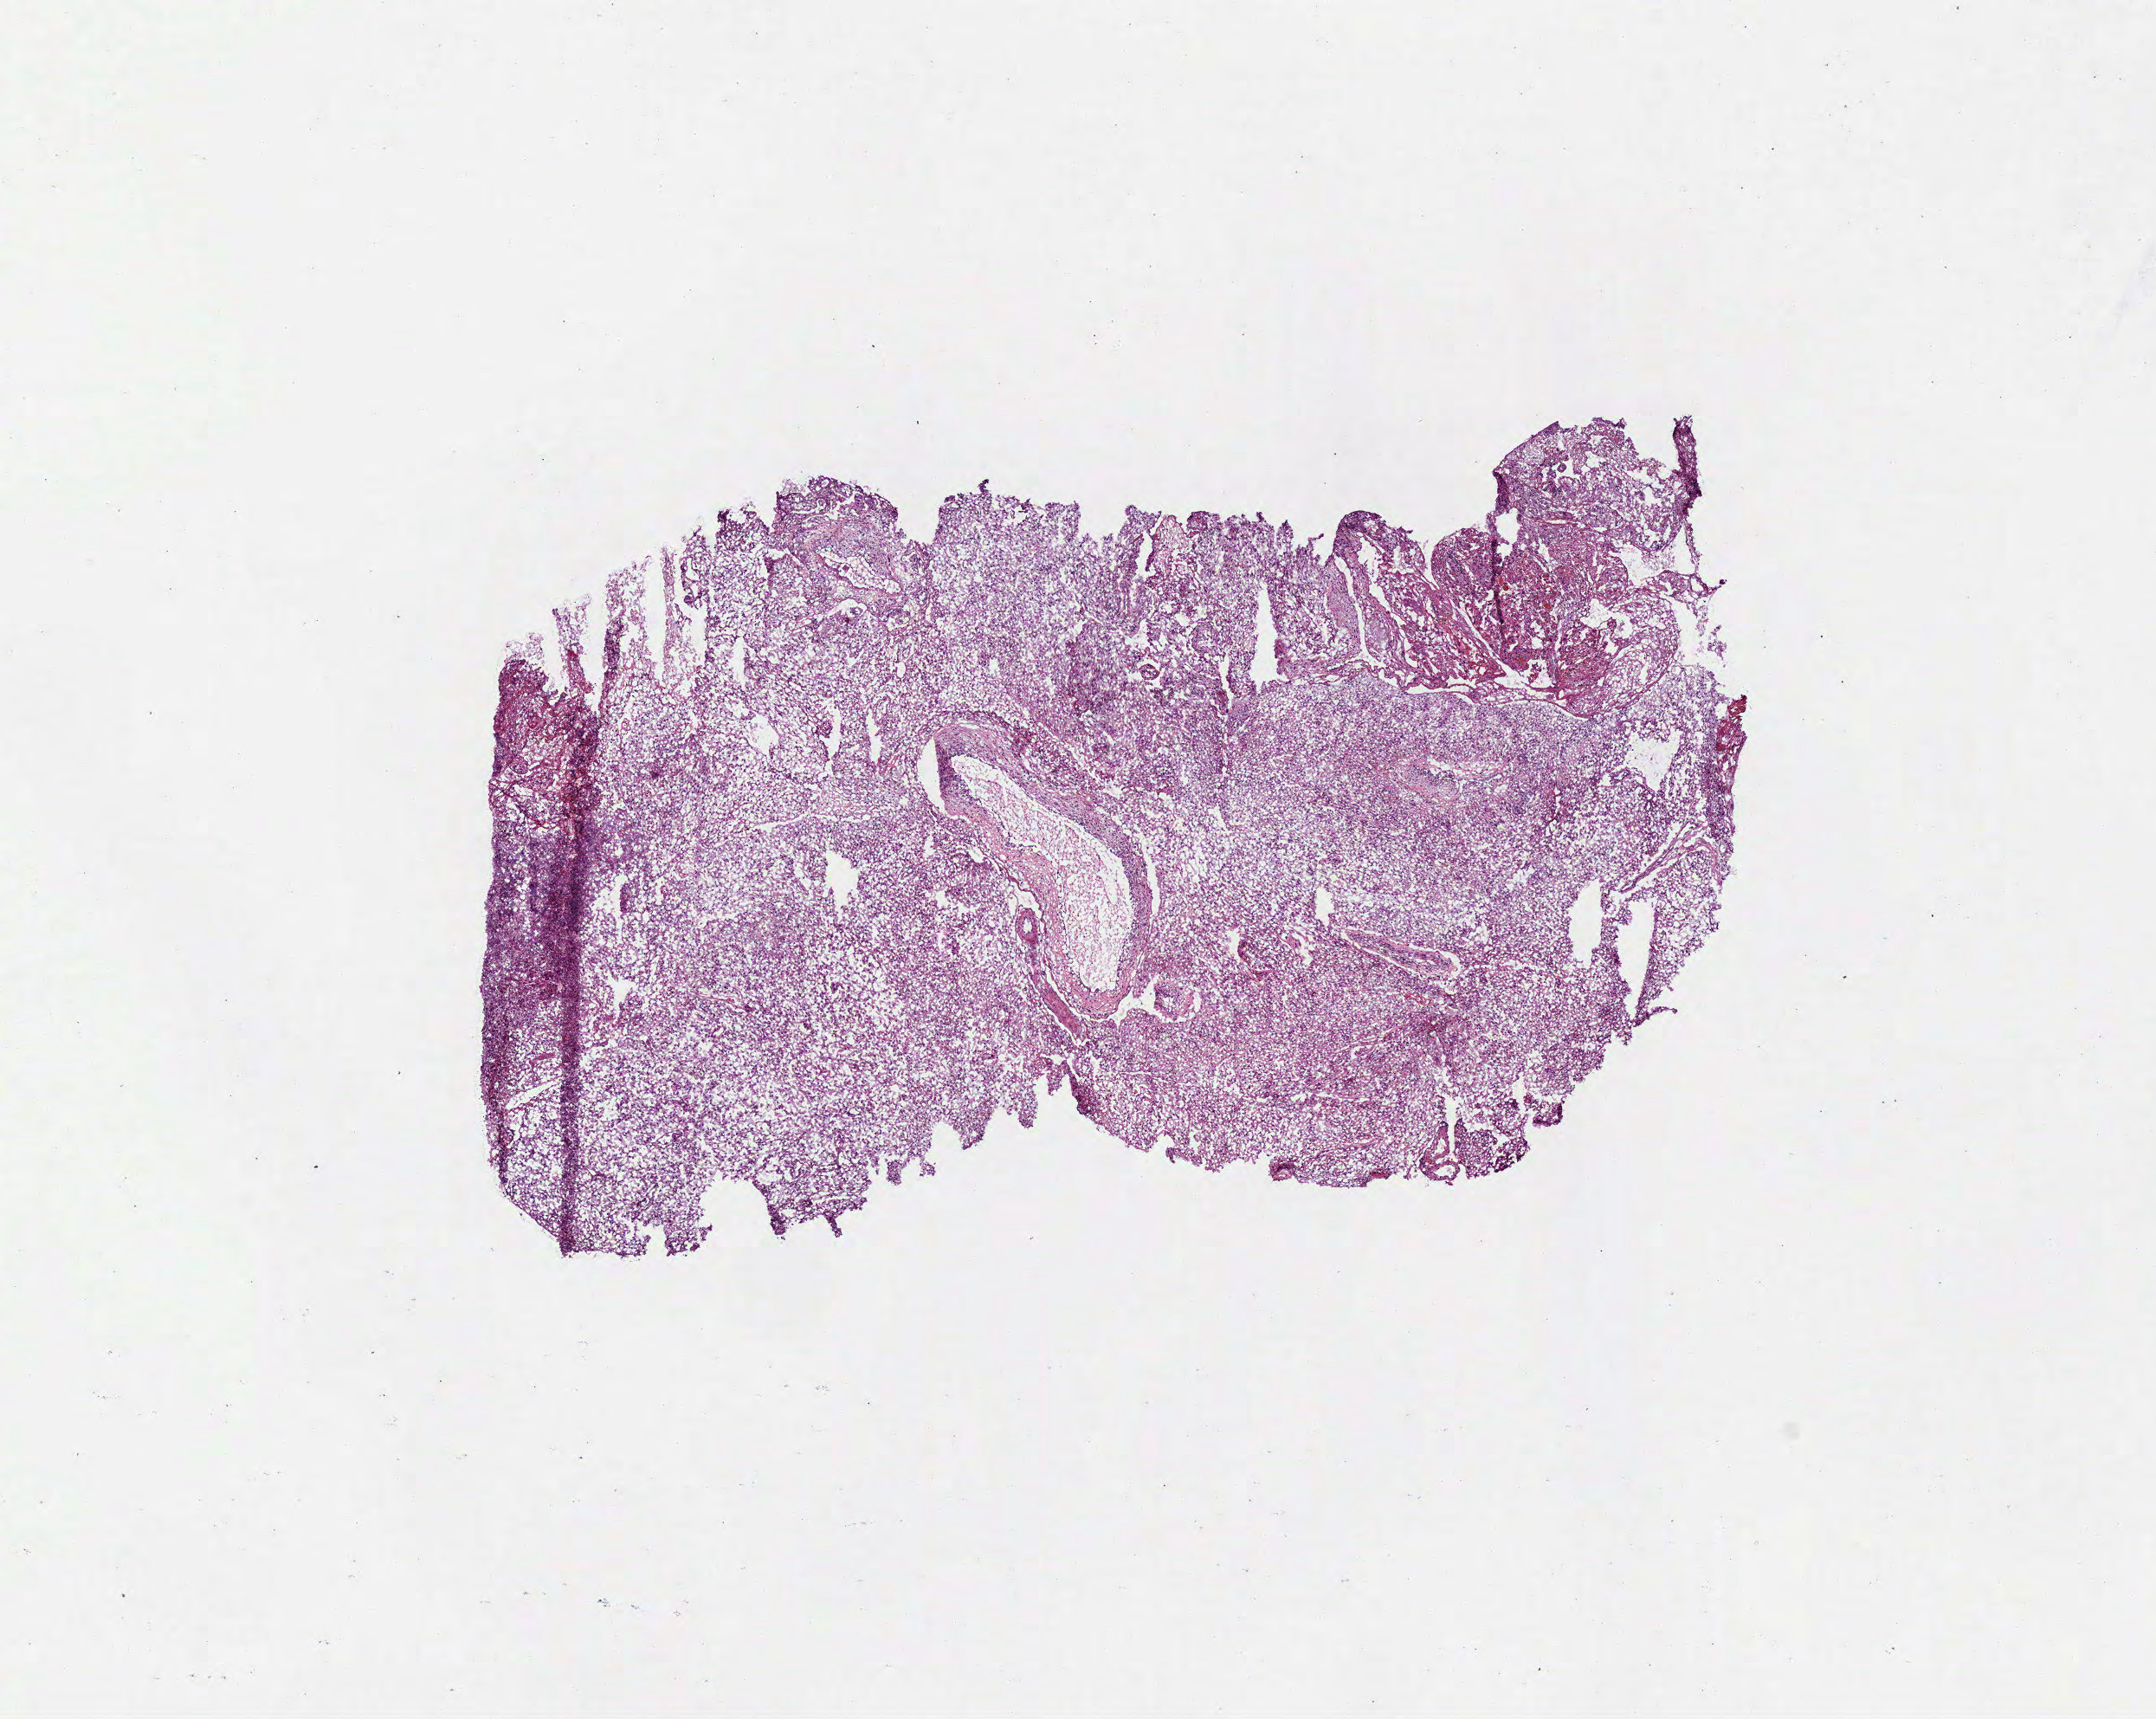
Digitized H&E tissue section (whole slide) — low-resolution overview of the scanned area, about 9.8 x 7.8 mm, frozen section, brain, primary tumour sample. Male patient; age at initial diagnosis 42 years. Composition of this section per pathologist review: tumour cells 85%, tumour nuclei 80%, normal cells 0%, stromal cells 10%, necrosis 5%.
Diagnosis: Glioblastoma.